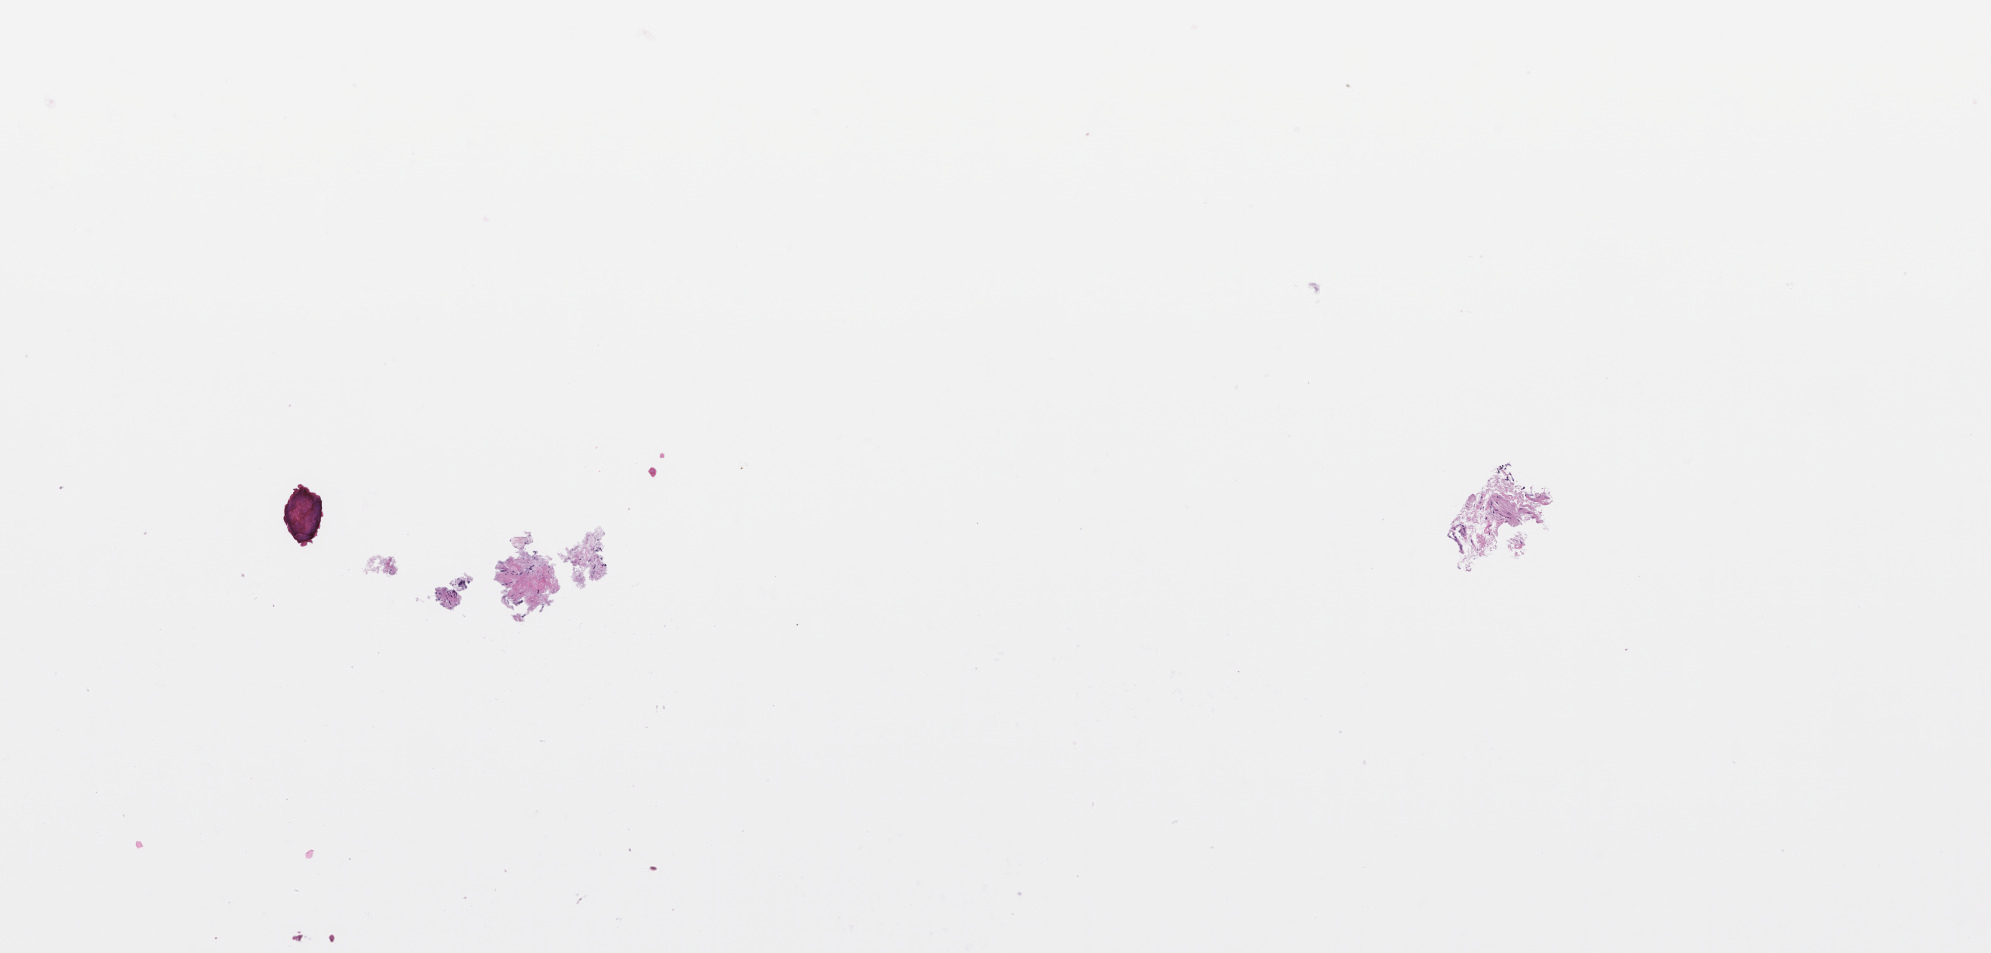
Hematoxylin and eosin (H&E) whole-slide image, a low-resolution overview of the entire scanned area, about 8.0 x 3.8 mm, formalin-fixed, paraffin-embedded (FFPE) tissue, tissue site: prostate. Patient sex: male.
- this section: primary tumor
- diagnosis: Prostate Carcinoma